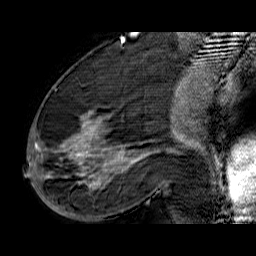
Breast MRI (dynamic contrast-enhanced), one sagittal slice; dynamic contrast-enhanced series, time point 2 of 6 at this slice position (early post-contrast); 1.5 T; TE 6.5 ms, TR 32.9 ms; 4 mm slice thickness; 256 × 256 image matrix, field of view 200 × 200 mm. Female patient. Case-level facts recorded for this patient, not image findings: setting: breast cancer imaged before/during neoadjuvant chemotherapy; receptor status: HR-positive, HER2-negative.
Outlined on this slice (semi-automatically segmented with operator editing):
- analysis volume of interest (the breast-tissue region the enhancement analysis was run in; not a lesion): box from (x=33, y=74) to (x=176, y=210) px
- tumour enhancement mask (voxels above the 100 % enhancement threshold inside the analysis volume of interest): (x=34, y=112)–(x=138, y=189)